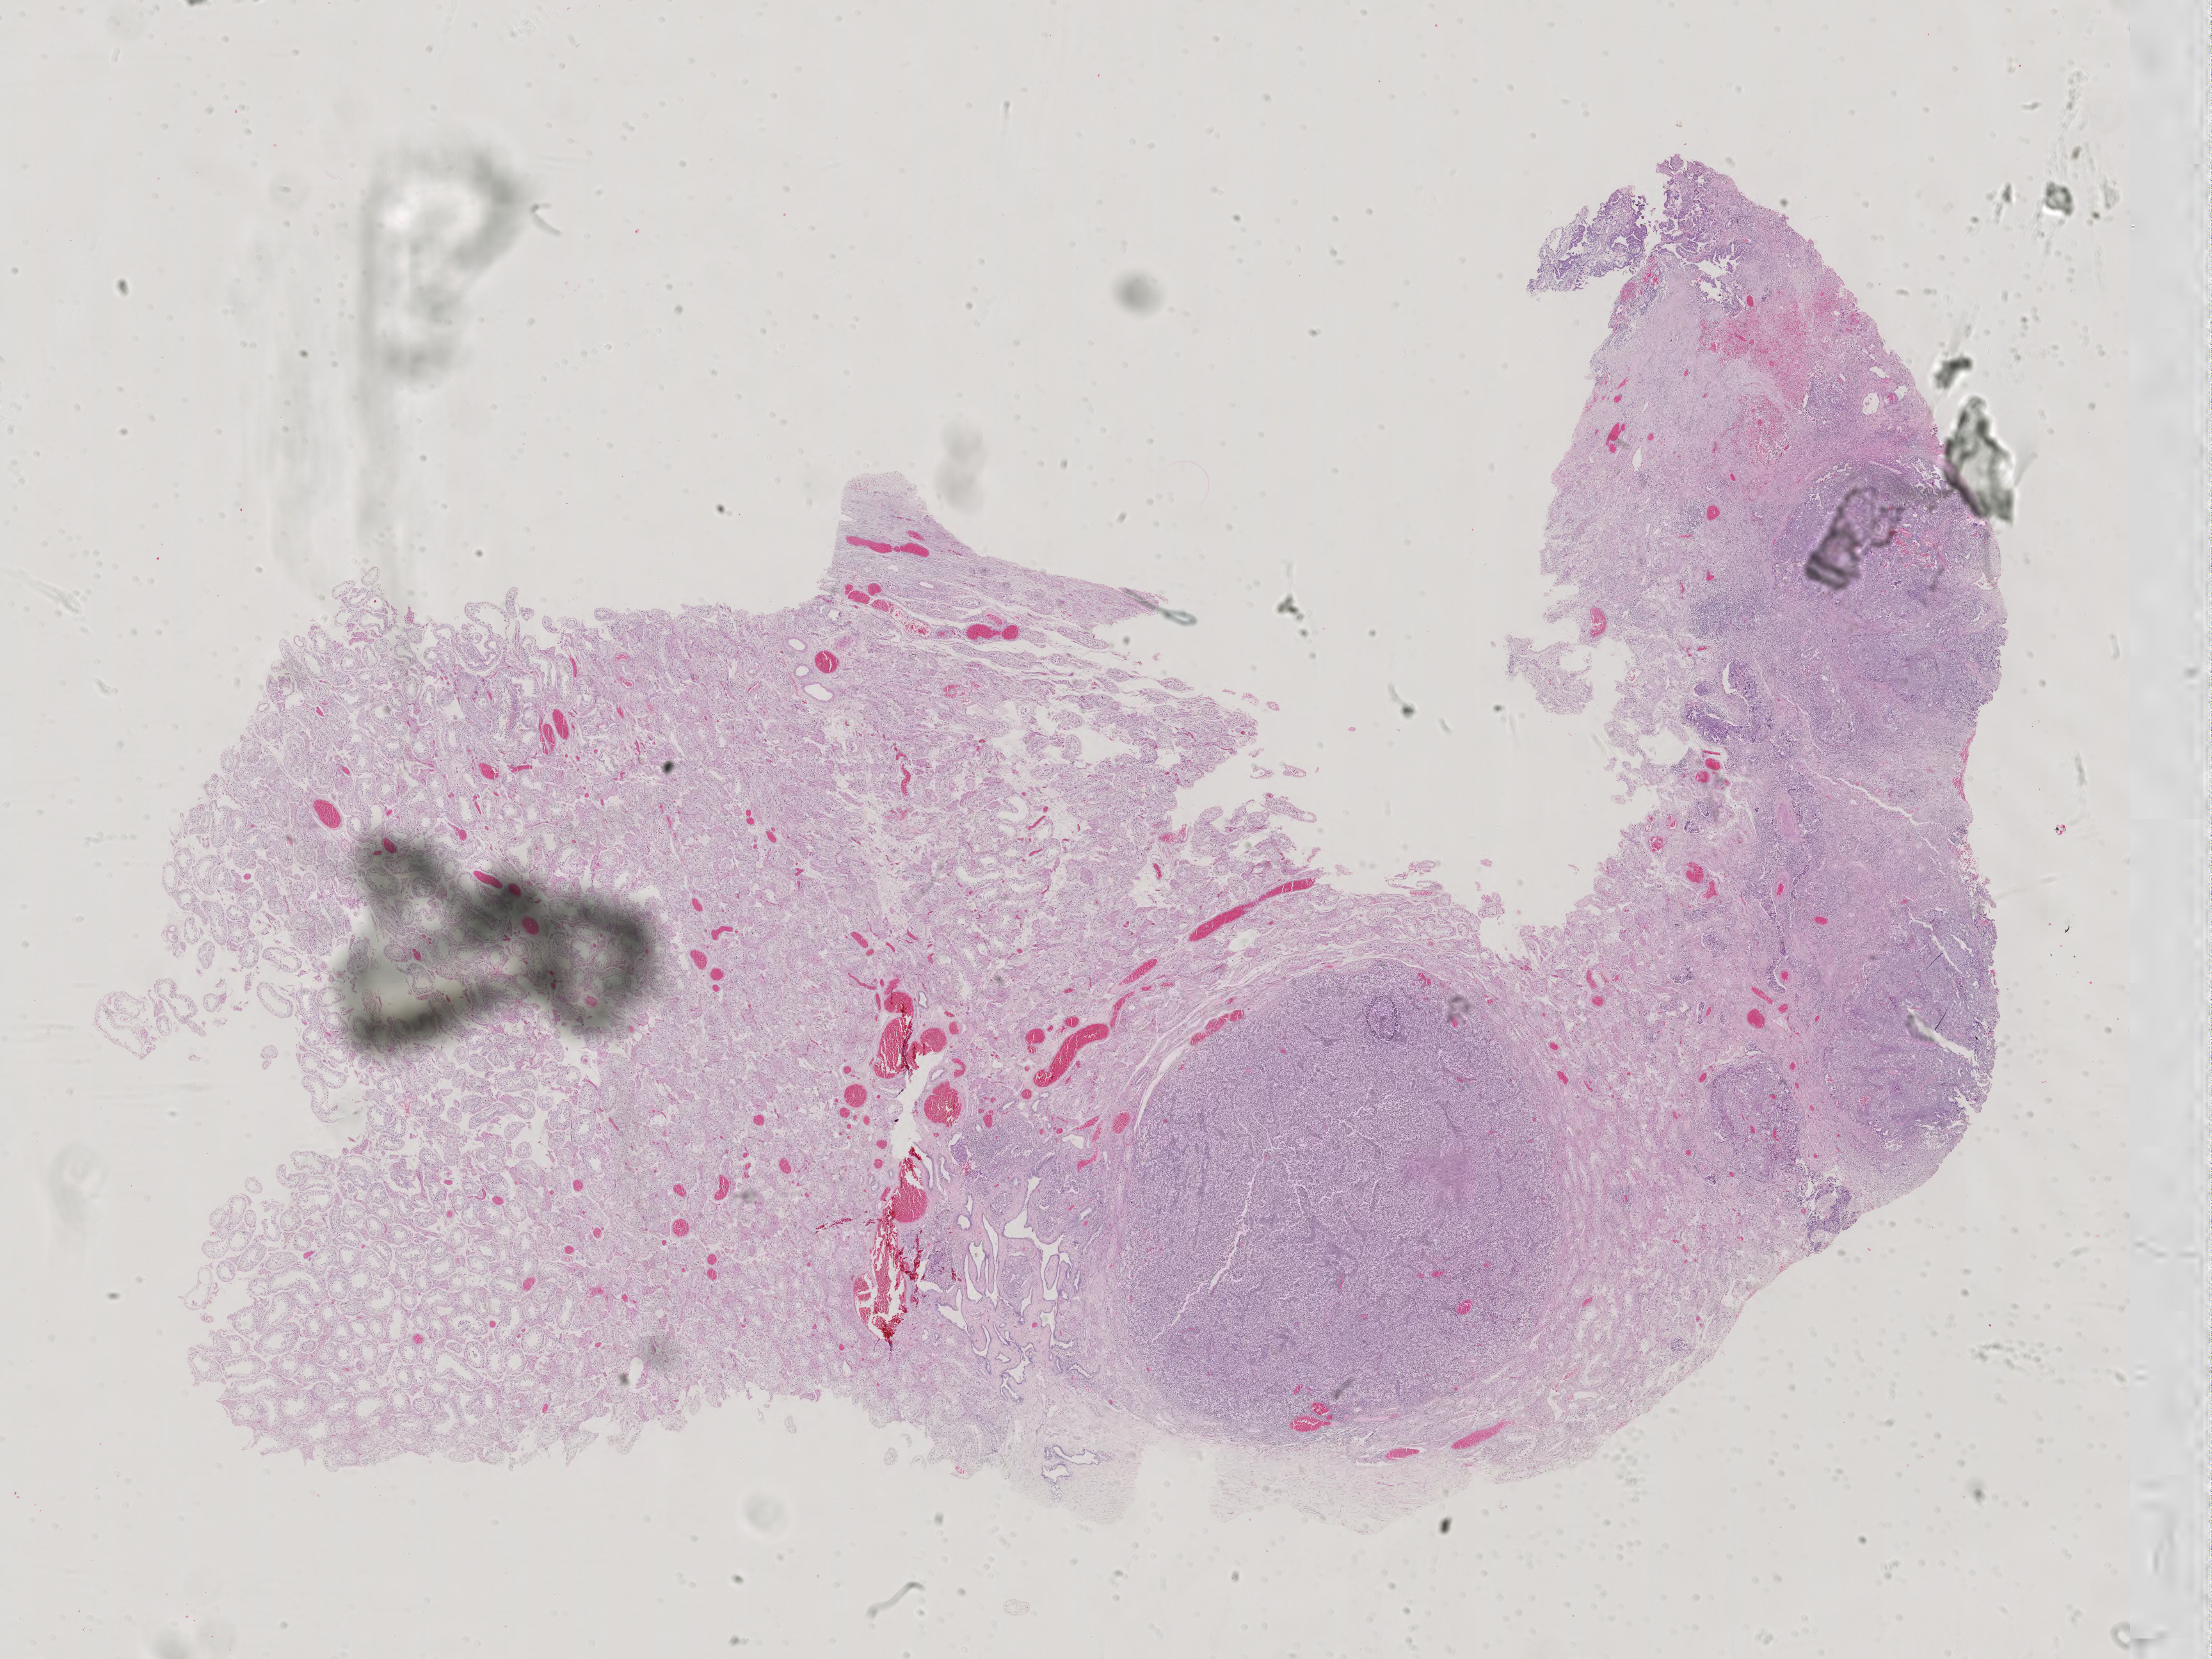
H&E-stained whole-slide image — a low-resolution overview of the entire scanned area, about 25.2 x 18.9 mm (acquisition: 40x scan), FFPE section, sample: primary tumour, testis. Male patient; age at initial diagnosis 28 years.
• histologic diagnosis: Mixed germ cell tumor
• AJCC pathologic stage: IS